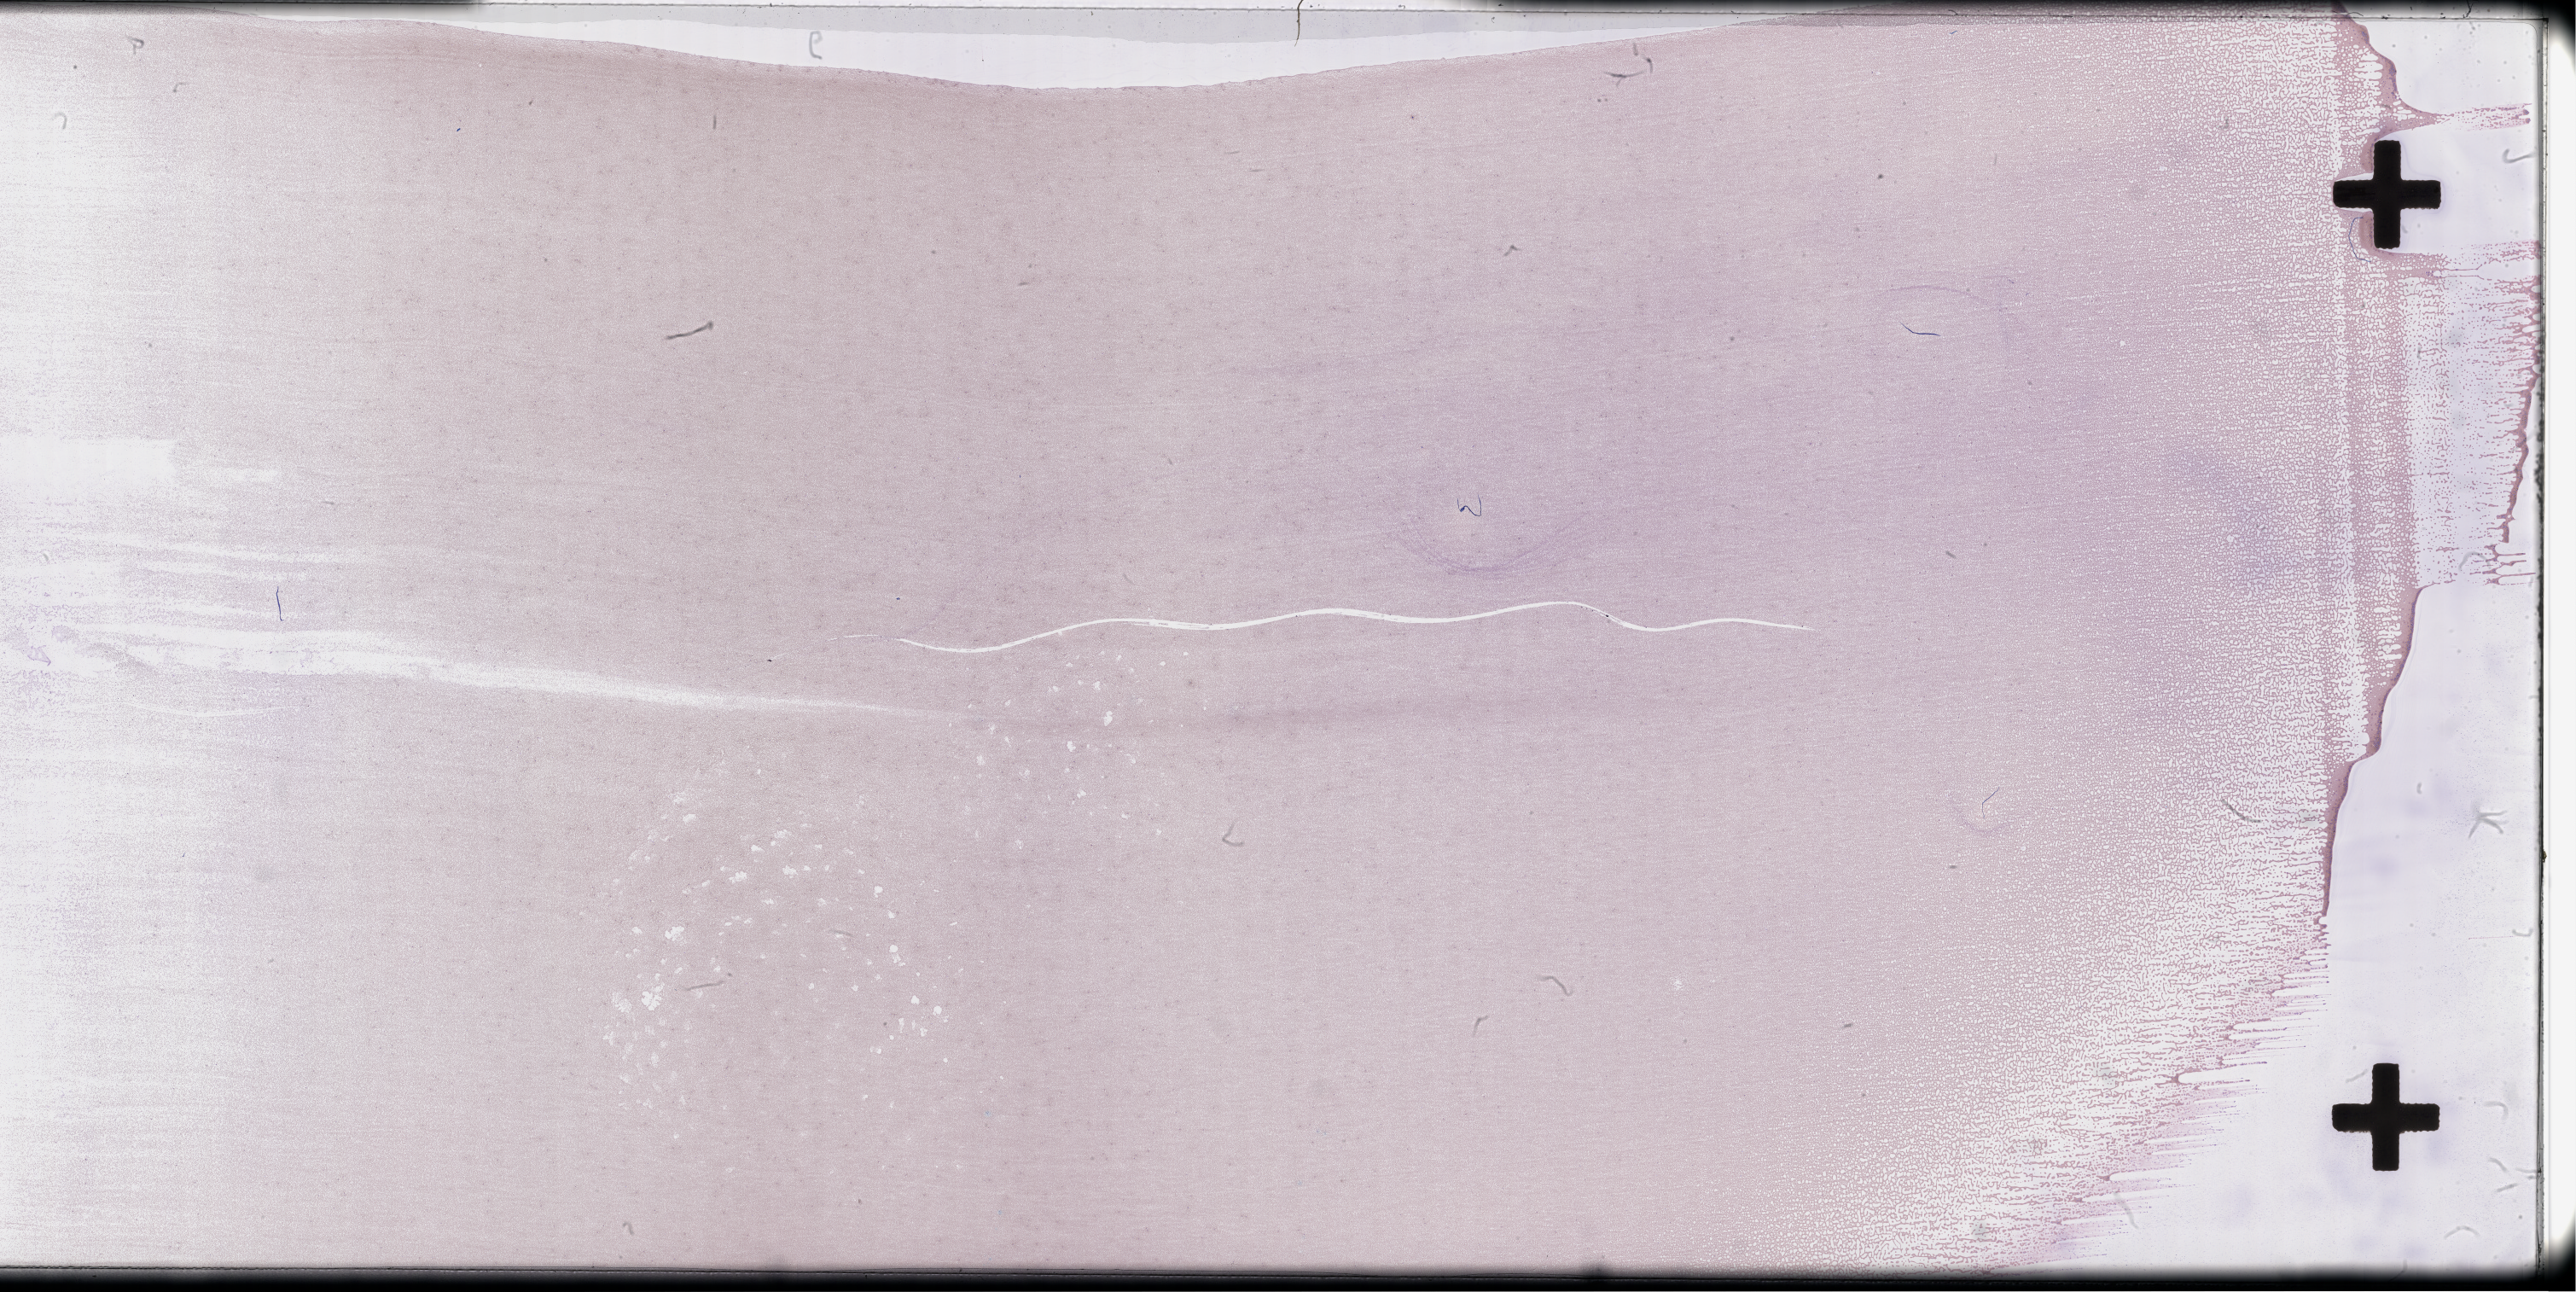
Wright–Giemsa-stained whole blood smear, whole-slide image, low-resolution overview of the scanned area, about 48.8 x 24.4 mm, collected on treatment. Patient: male.
• patient diagnosis: Plasma Cell Myeloma